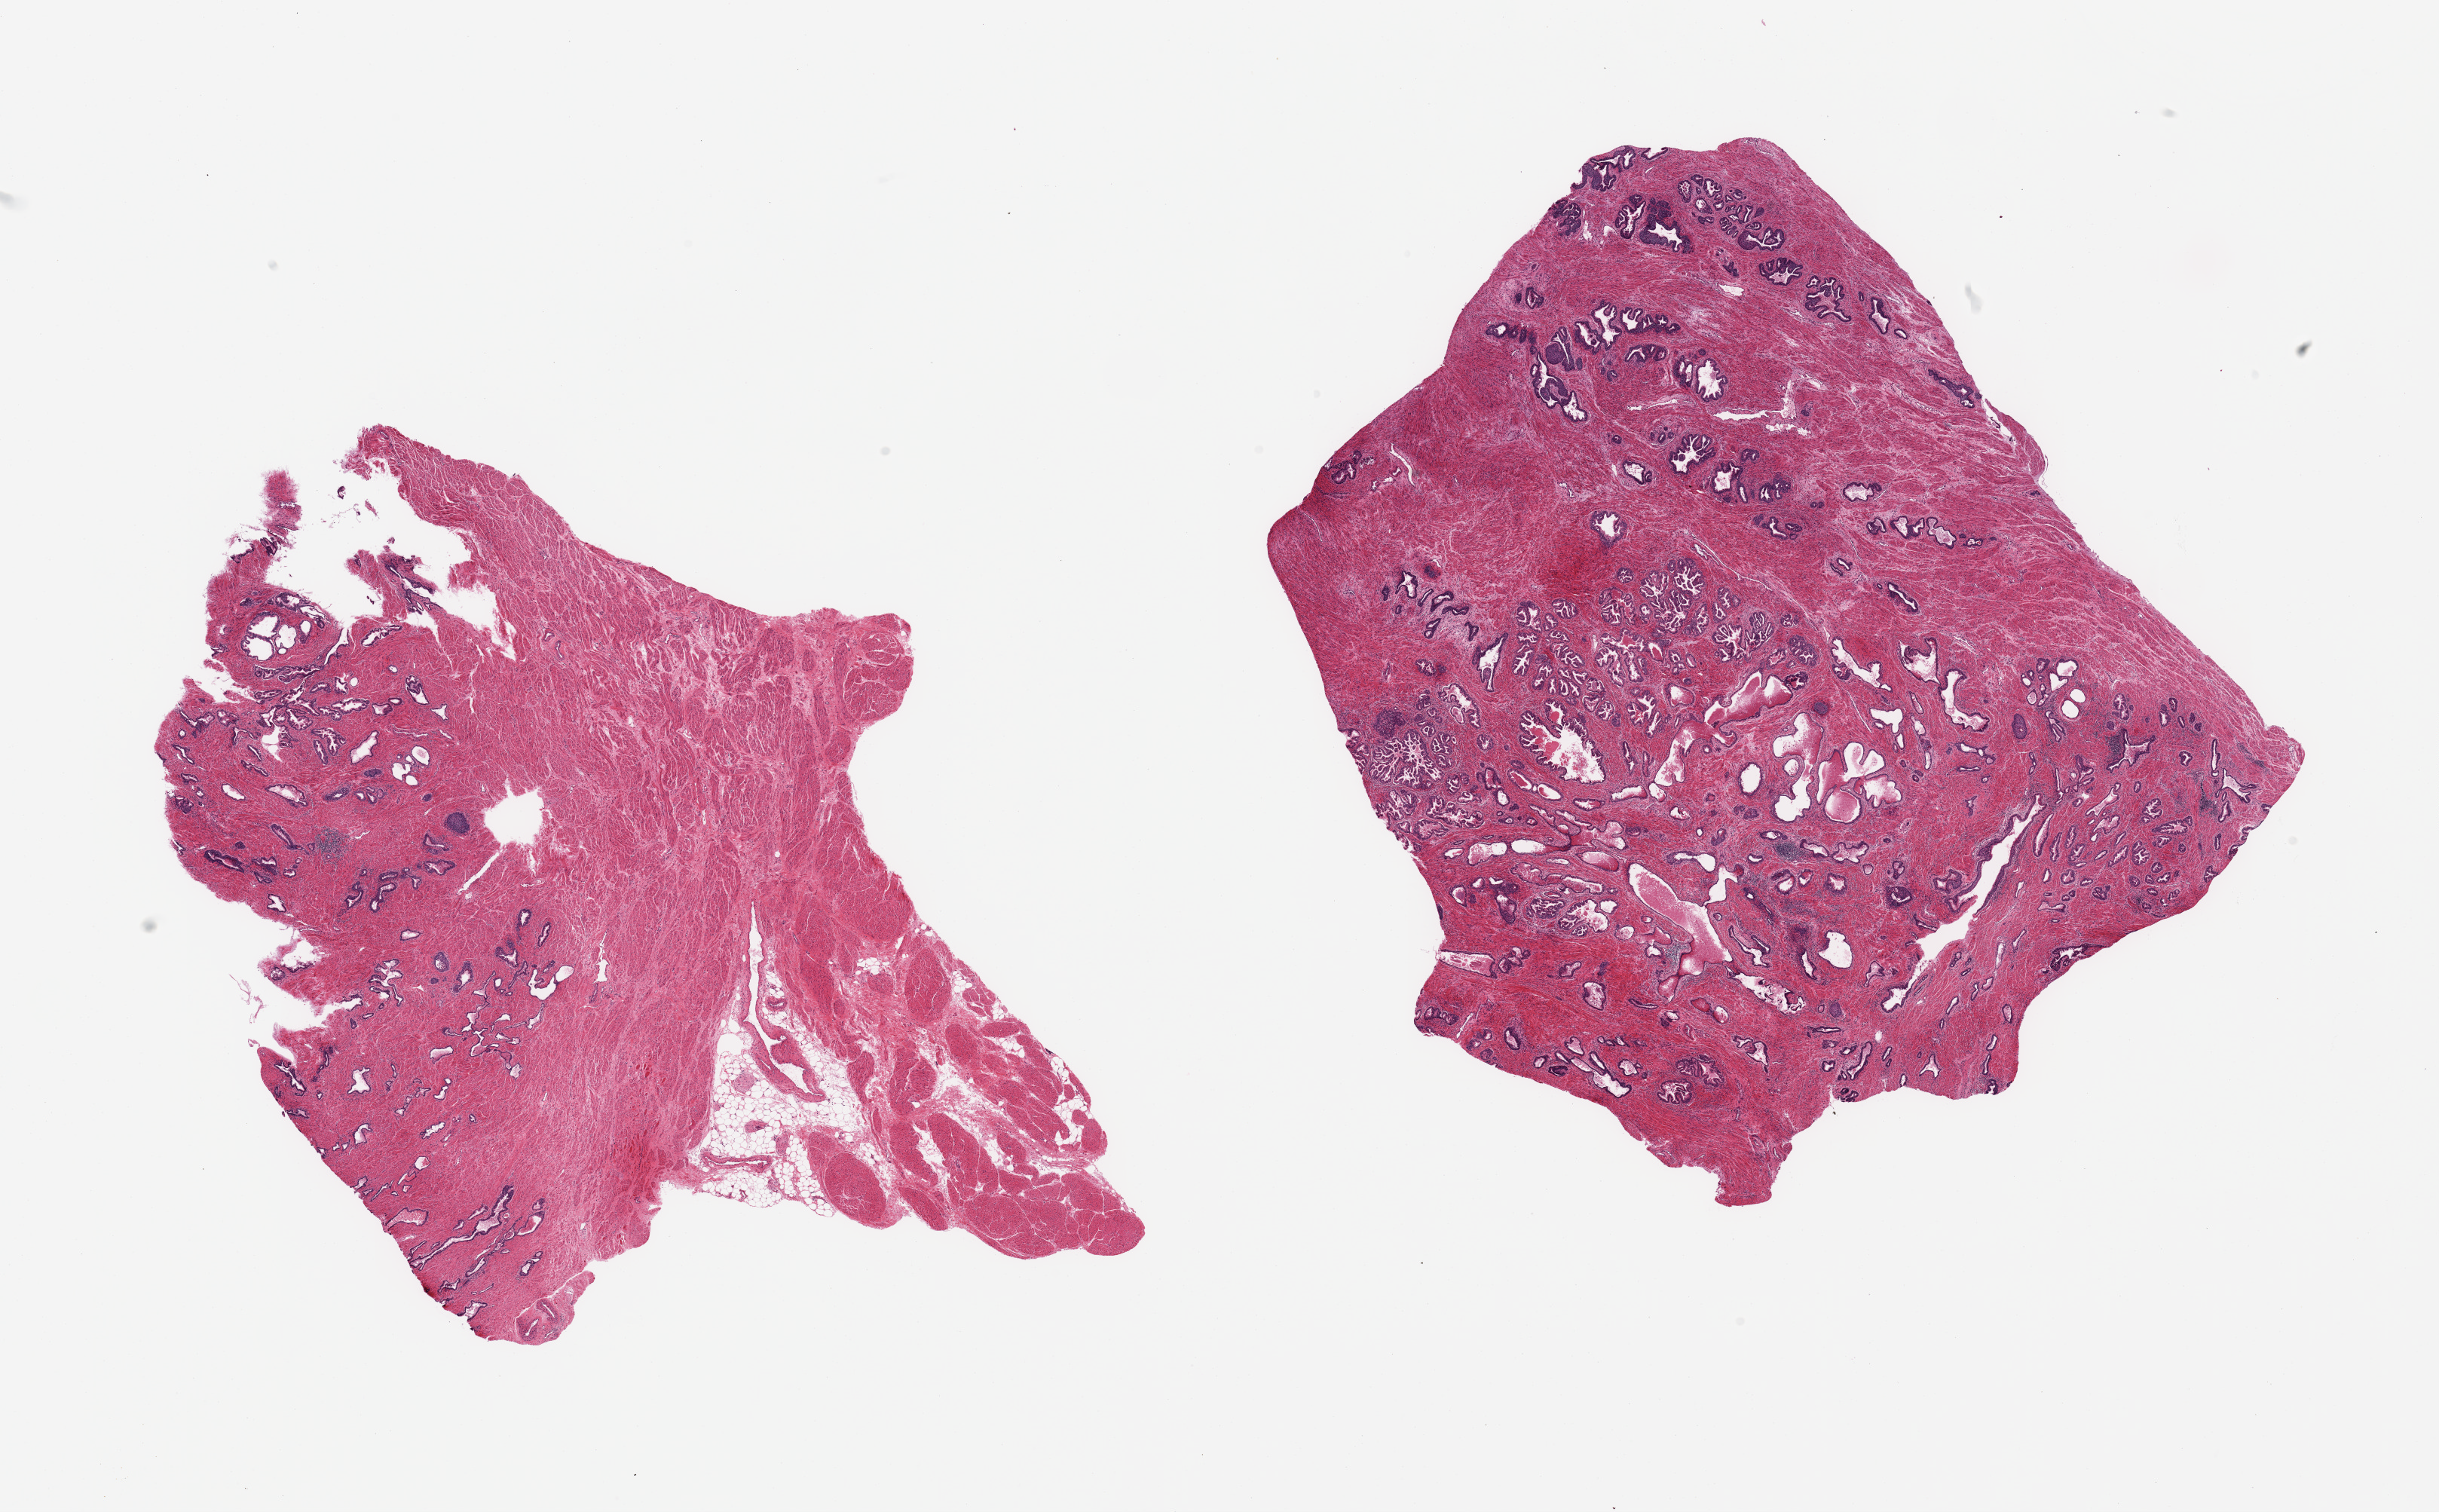
H&E whole-slide image — a low-resolution overview of the entire scanned area, about 25.6 x 15.9 mm; PAXgene-fixed, paraffin-embedded tissue; target tissue: prostate; donor tissue sample. Male donor.
Pathologist's review note for this sample: 2 pieces; 1 piece has over 50% muscle content.